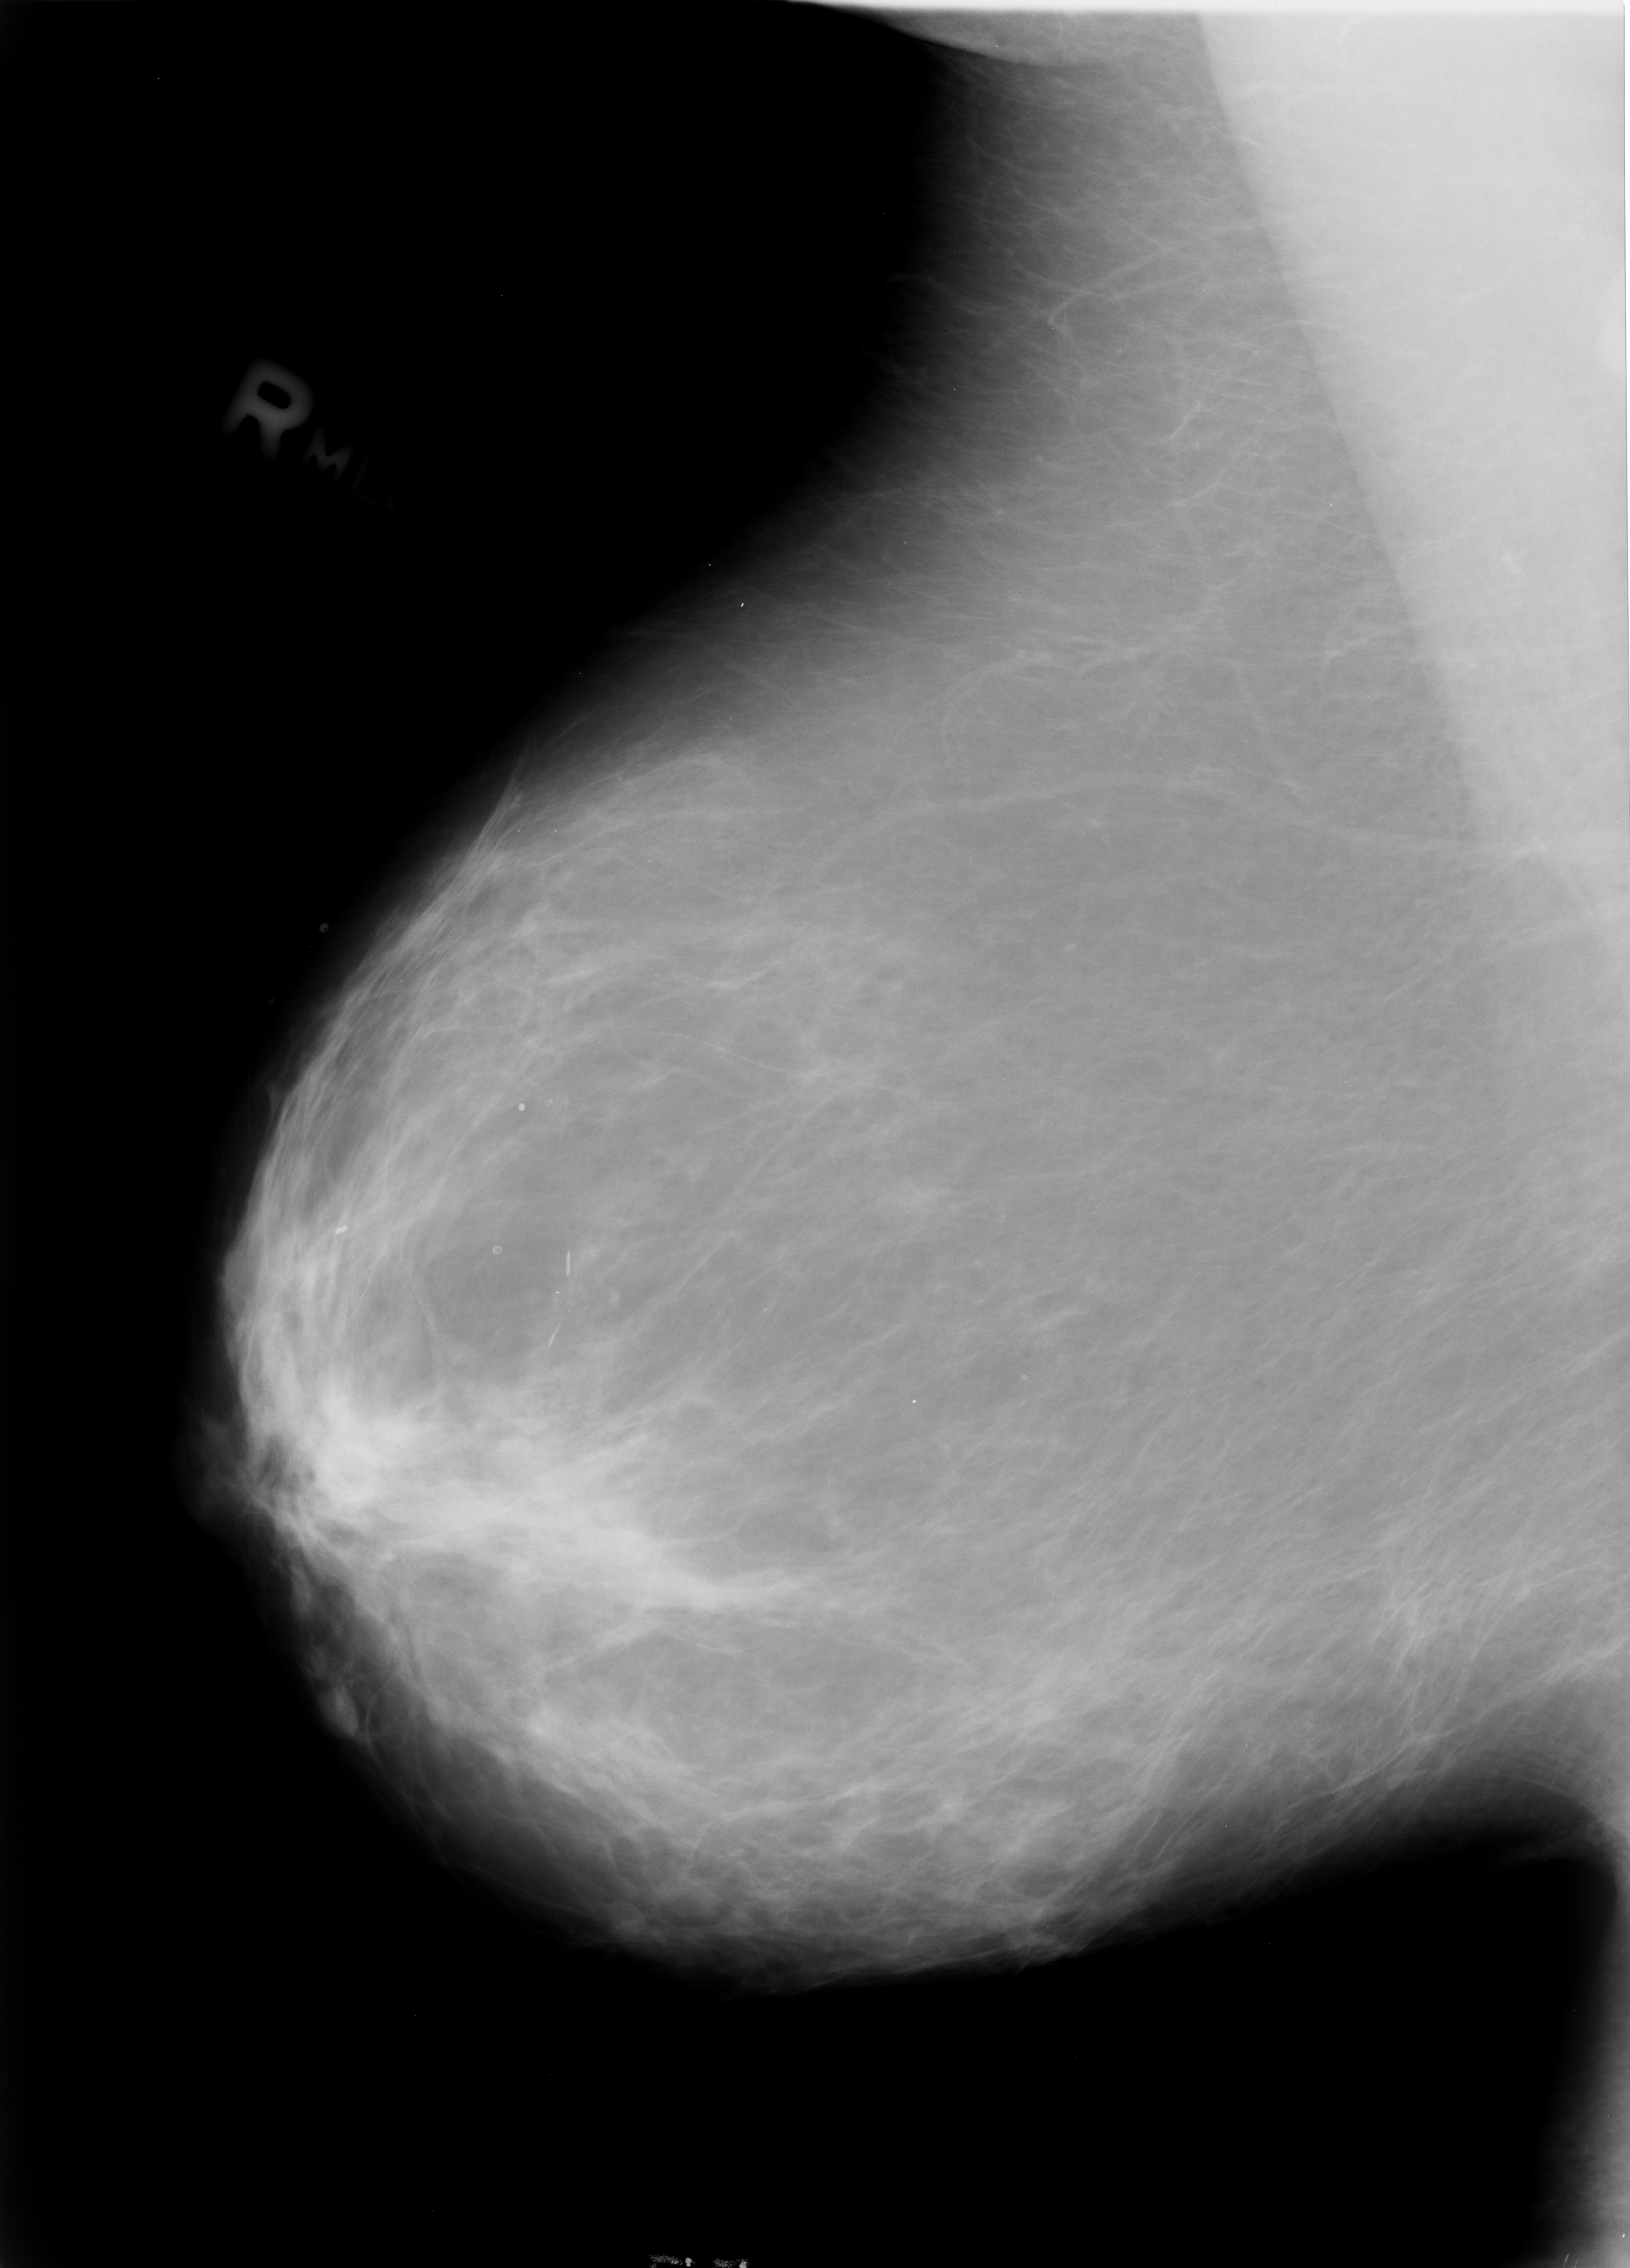
Scanned film-screen mammogram; right breast; MLO view; BI-RADS breast density category 2 (scale 1–4).
Radiologist-marked abnormalities on this image: calcifications, morphology amorphous / pleomorphic, distribution clustered; BI-RADS assessment category 4; subtlety rating 2 on a 1 (subtle) to 5 (obvious) scale; pathology result (as recorded, not read from the image): benign.